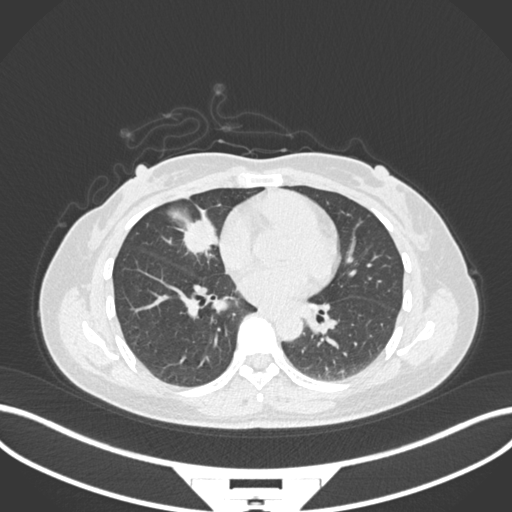
Chest CT, one axial slice. 120 kVp. Lung window (W 1500 / L -600 HU). 1 mm slice thickness. 512 × 512 image matrix. Patient: female, 43 years. From the clinical record (not read from this slice): clinical TNM (as recorded): T1c N3 M1; histopathological grade: G1.
Structures marked on this image (bounding box drawn by a radiologist):
- lung tumour (recorded histology: adenocarcinoma): bounding box <176,216,223,259> (left, top, right, bottom; pixels)